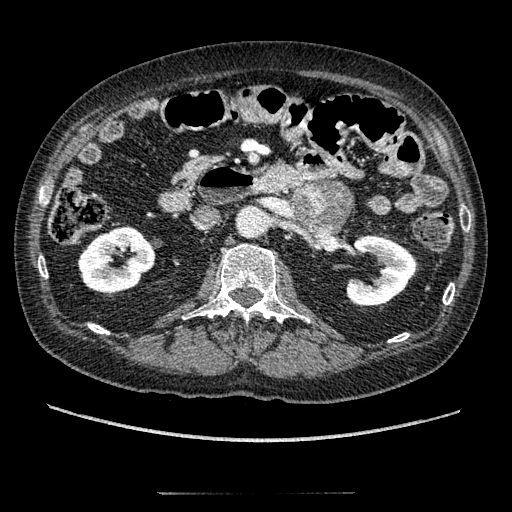
Contrast-enhanced abdominal CT, one axial slice. Slice 87 of 274 in the series (ordered by position). 120 kVp. Soft-tissue window (W 400 / L 40 HU). 1.25 mm slice thickness. 512 × 512 image matrix, field of view 381 × 381 mm. Patient: male, 69 years. Case-level facts recorded for this patient, not image findings: diagnosis: adrenocortical carcinoma; tumour side: left adrenal; tumour size at pathology: 6.1 cm; Ki-67 index: 10 %; stage (as recorded): 3.
Annotated regions visible in this slice (semi-automatic segmentation, software-assisted and operator-edited):
- mass: box from (x=293, y=182) to (x=351, y=230) px